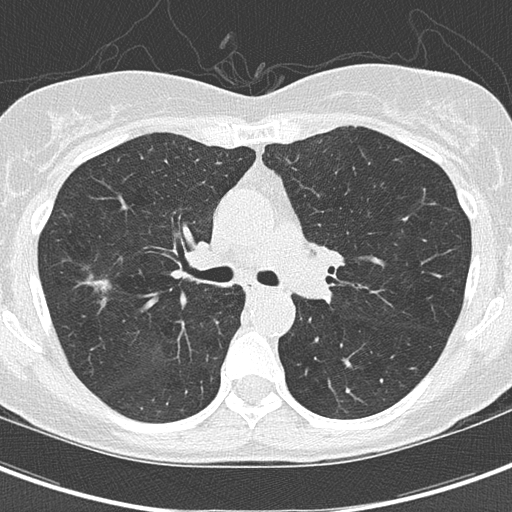
Low-dose screening chest CT, axial slice. Third screening round (two years after baseline). Lung window (W 1500 / L -600 HU). 120 kVp. Female, age 59 years at enrolment. Current smoker at enrolment.
Expert reader's lesion annotation, bounding box [x1, y1, x2, y2] px = [71, 261, 130, 315]. Reader record for this screening exam (exam-level; its link to the box is not recorded): non-calcified nodule or mass ≥4 mm, right upper lobe, 10 × 8 mm, poorly defined margins, ground glass attenuation, pre-existing on the prior screen: yes; interval growth: yes. Participant outcome: lung cancer diagnosed 63 days after this screen — bronchiolo-alveolar adenocarcinoma, NOS, right upper lobe, well differentiated (G1), stage IA (AJCC 6th edition), 4 mm at pathology.